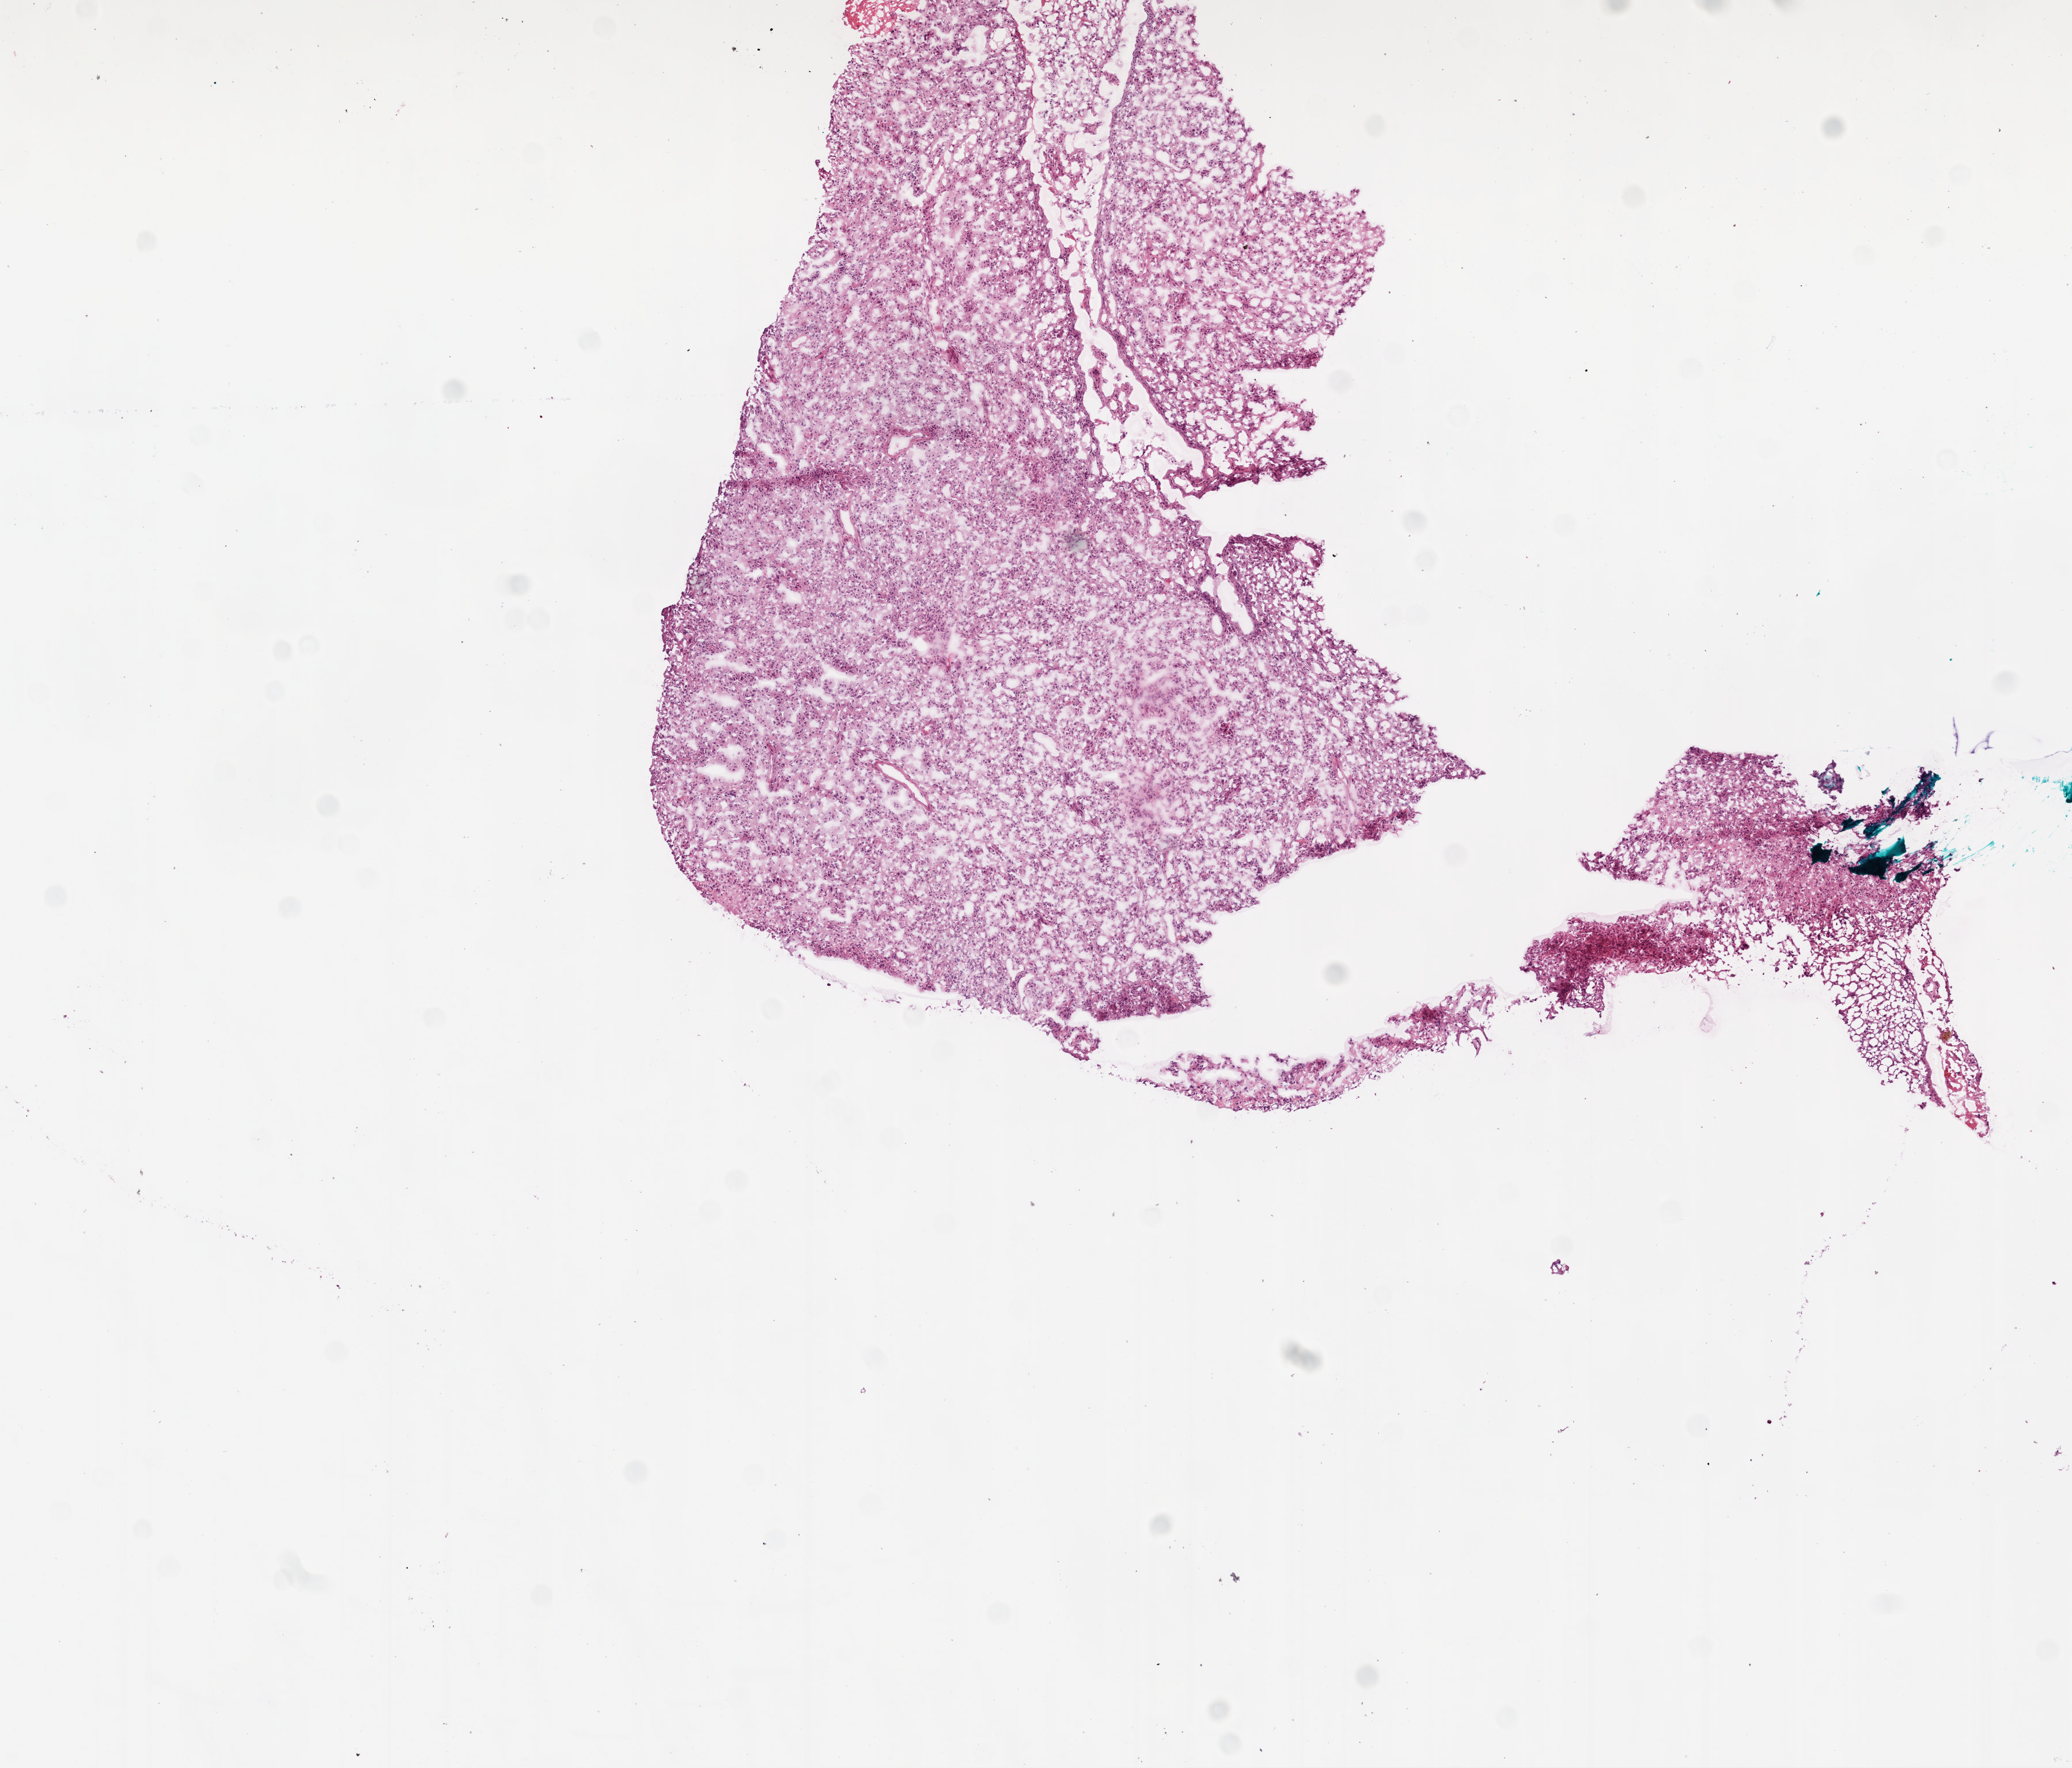
Digitized H&E-stained tissue section (whole slide) — whole scanned area (about 7.3 x 6.2 mm, slide scanned at 20x) shown as a low-resolution overview; frozen section; primary tumour sample from the brain. Female patient; age at initial diagnosis 48 years. Slide review estimates, as recorded: tumour cells 95%, tumour nuclei 100%, normal cells 0%, stromal cells 0%, necrosis 5%.
* diagnosis: Glioblastoma